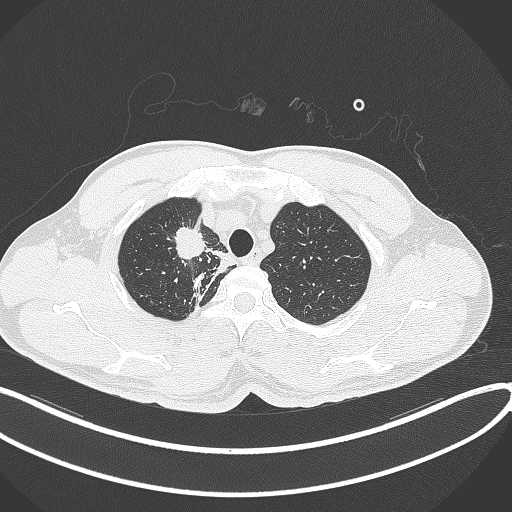
Chest CT, one axial slice; position 321 of 391 along the scan axis; 120 kVp; lung window (W 1500 / L -600 HU); 1 mm slice thickness; 512 × 512 image matrix, field of view 400 × 400 mm. Patient: male, 48 years. From the clinical record (not read from this slice): clinical TNM (as recorded): T1c N1 M1.
Outlined on this slice (rectangle marked by the reading radiologist):
- lung tumour (recorded histology: adenocarcinoma): bounding box [x1, y1, x2, y2] px = [171, 222, 210, 260]